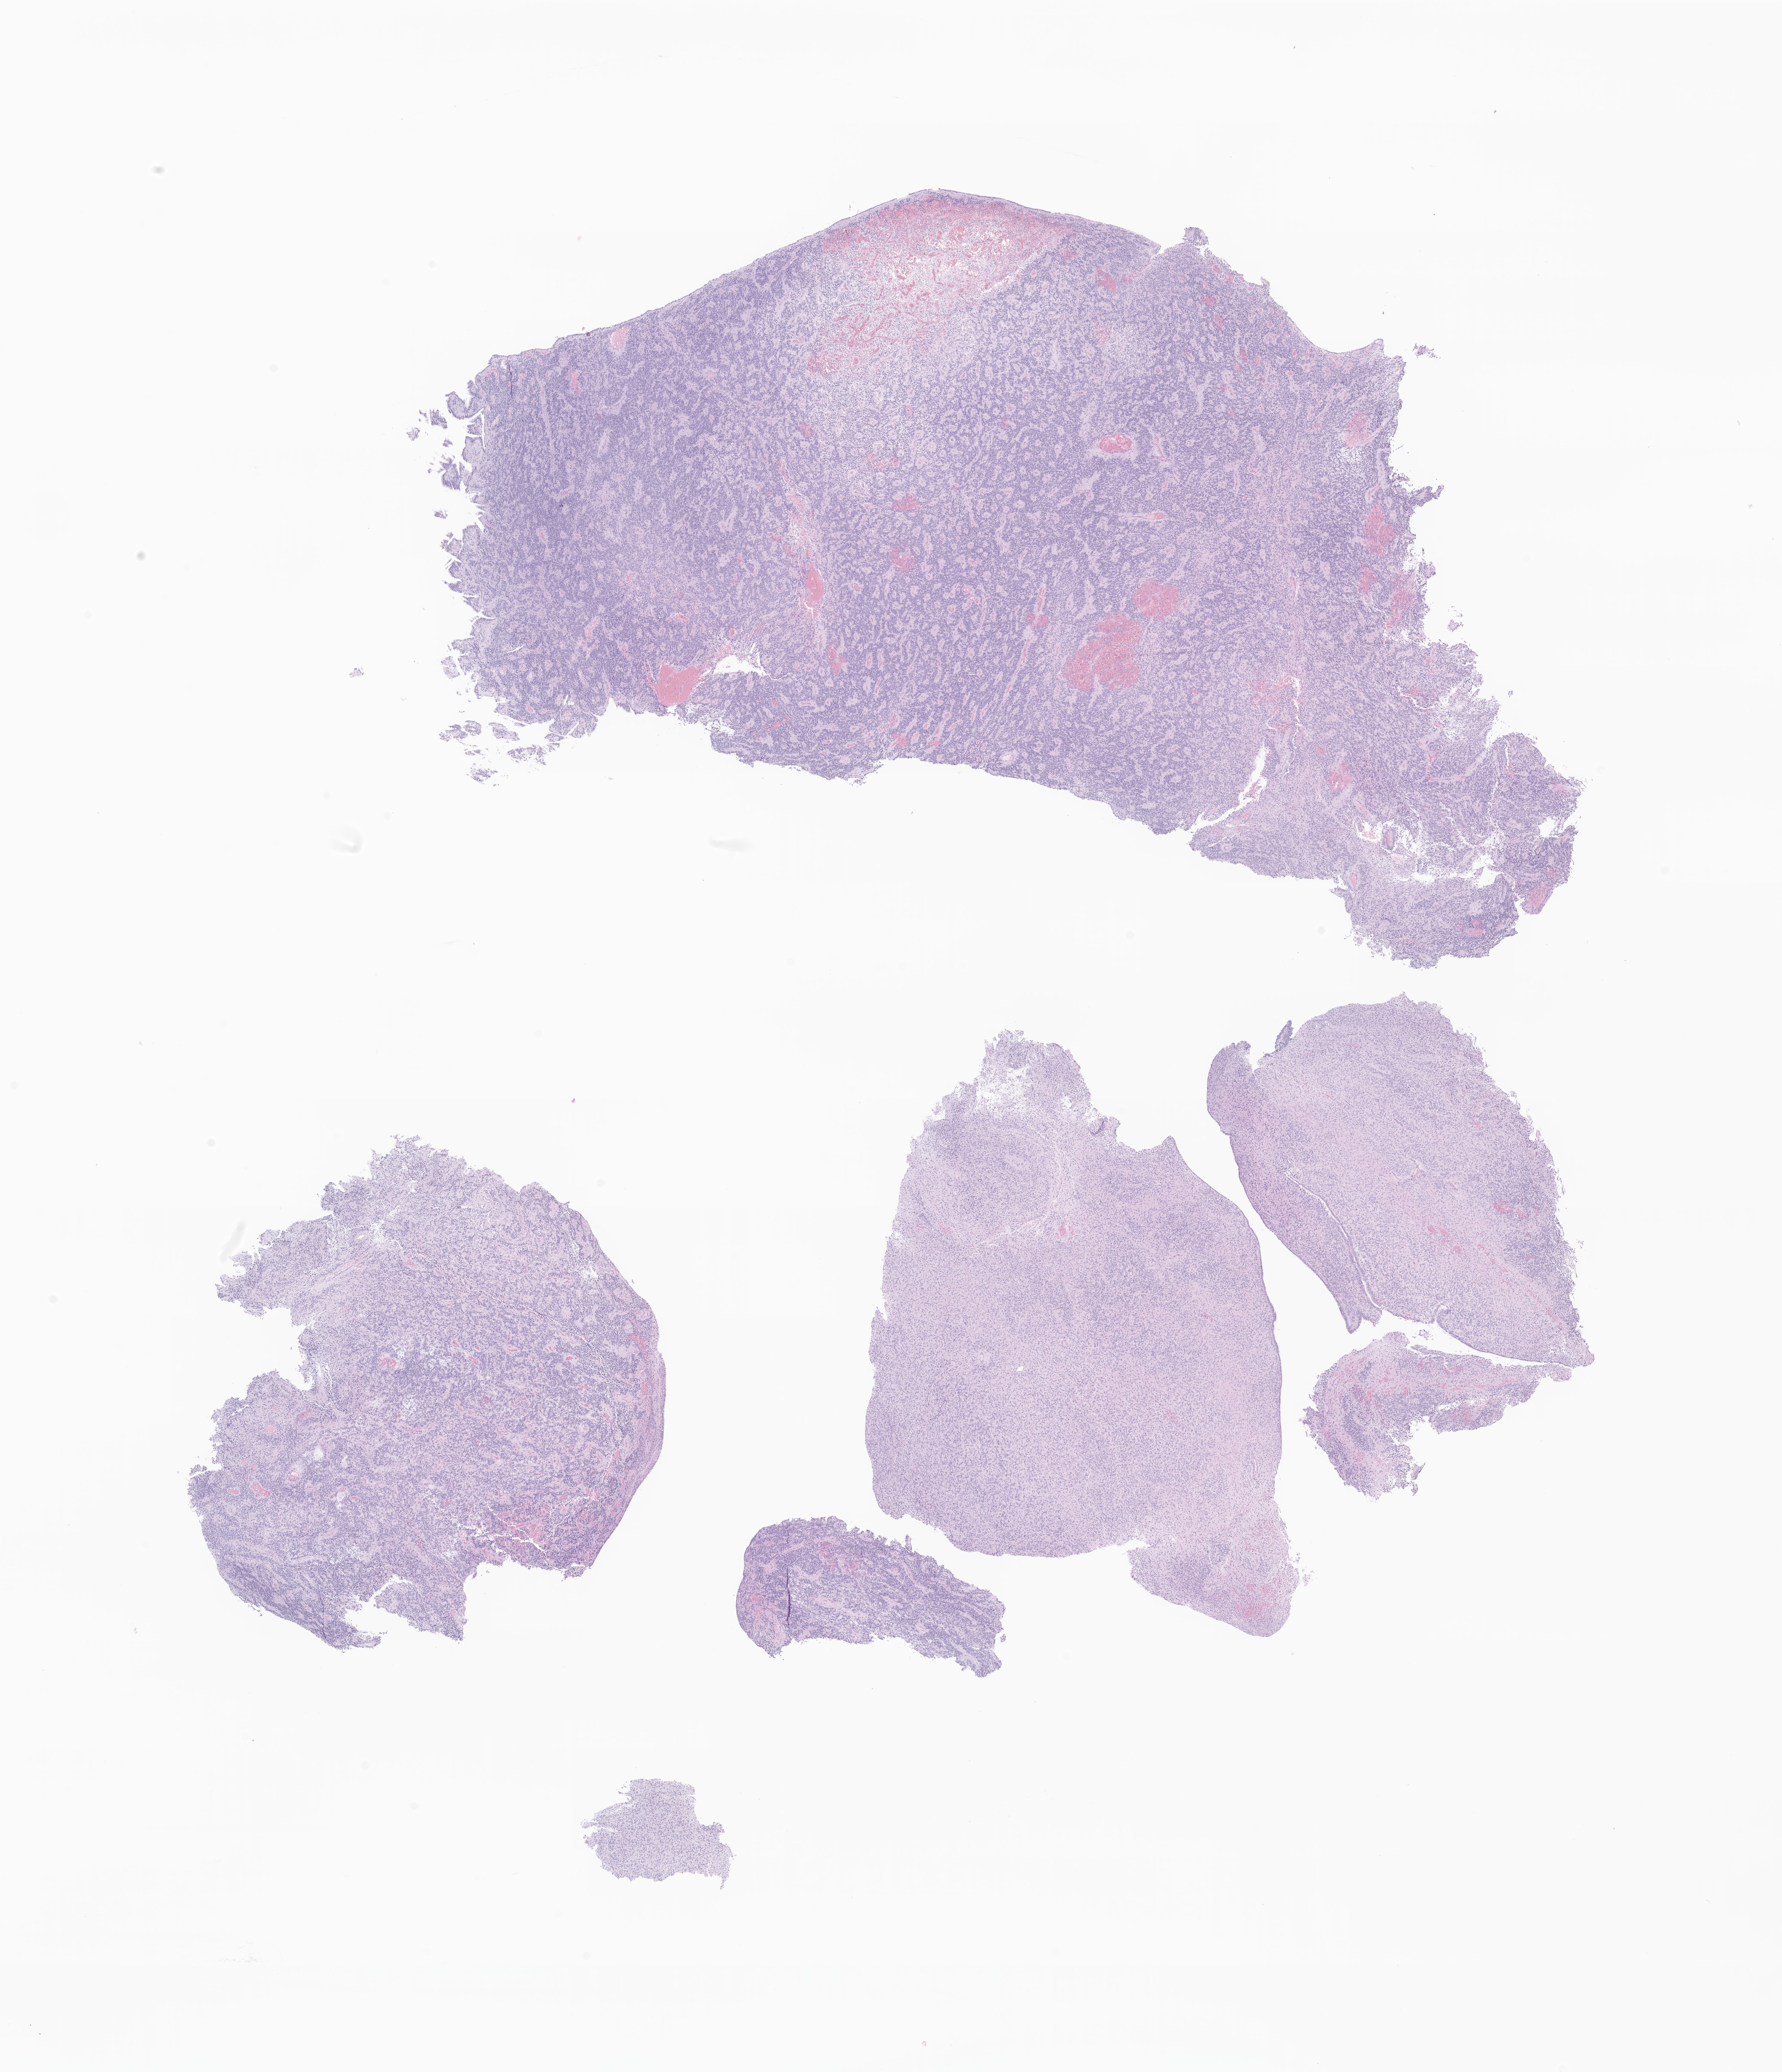
H&E whole-slide image of tumor tissue from the brain — whole scanned area (about 17.6 x 20.4 mm) shown as a low-resolution overview, FFPE section. Patient: male, age 709 days (about 1.9 years).
- diagnosis: Neoplasm, uncertain whether benign or malignant